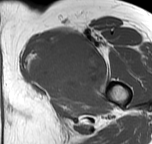
MRI of an extremity soft-tissue mass, one axial slice; slice 42 of 57 in the series (ordered by position); MR volume resampled by the dataset authors to the PET/CT grid (not the native acquisition matrix); 3.27 mm slice thickness; 152 × 144 image matrix. Female patient. Case-level facts recorded for this patient, not image findings: histological type: pleiomorphic leiomyosarcoma; grade: intermediate; site of the primary tumour: left thigh.
Structures marked on this image (expert contour drawn on MRI and transferred to this co-registered scan by the dataset authors):
- gross tumour volume including surrounding oedema: box from (x=27, y=31) to (x=99, y=91) px
- gross tumour volume (mass): (x=27, y=31)–(x=99, y=91)